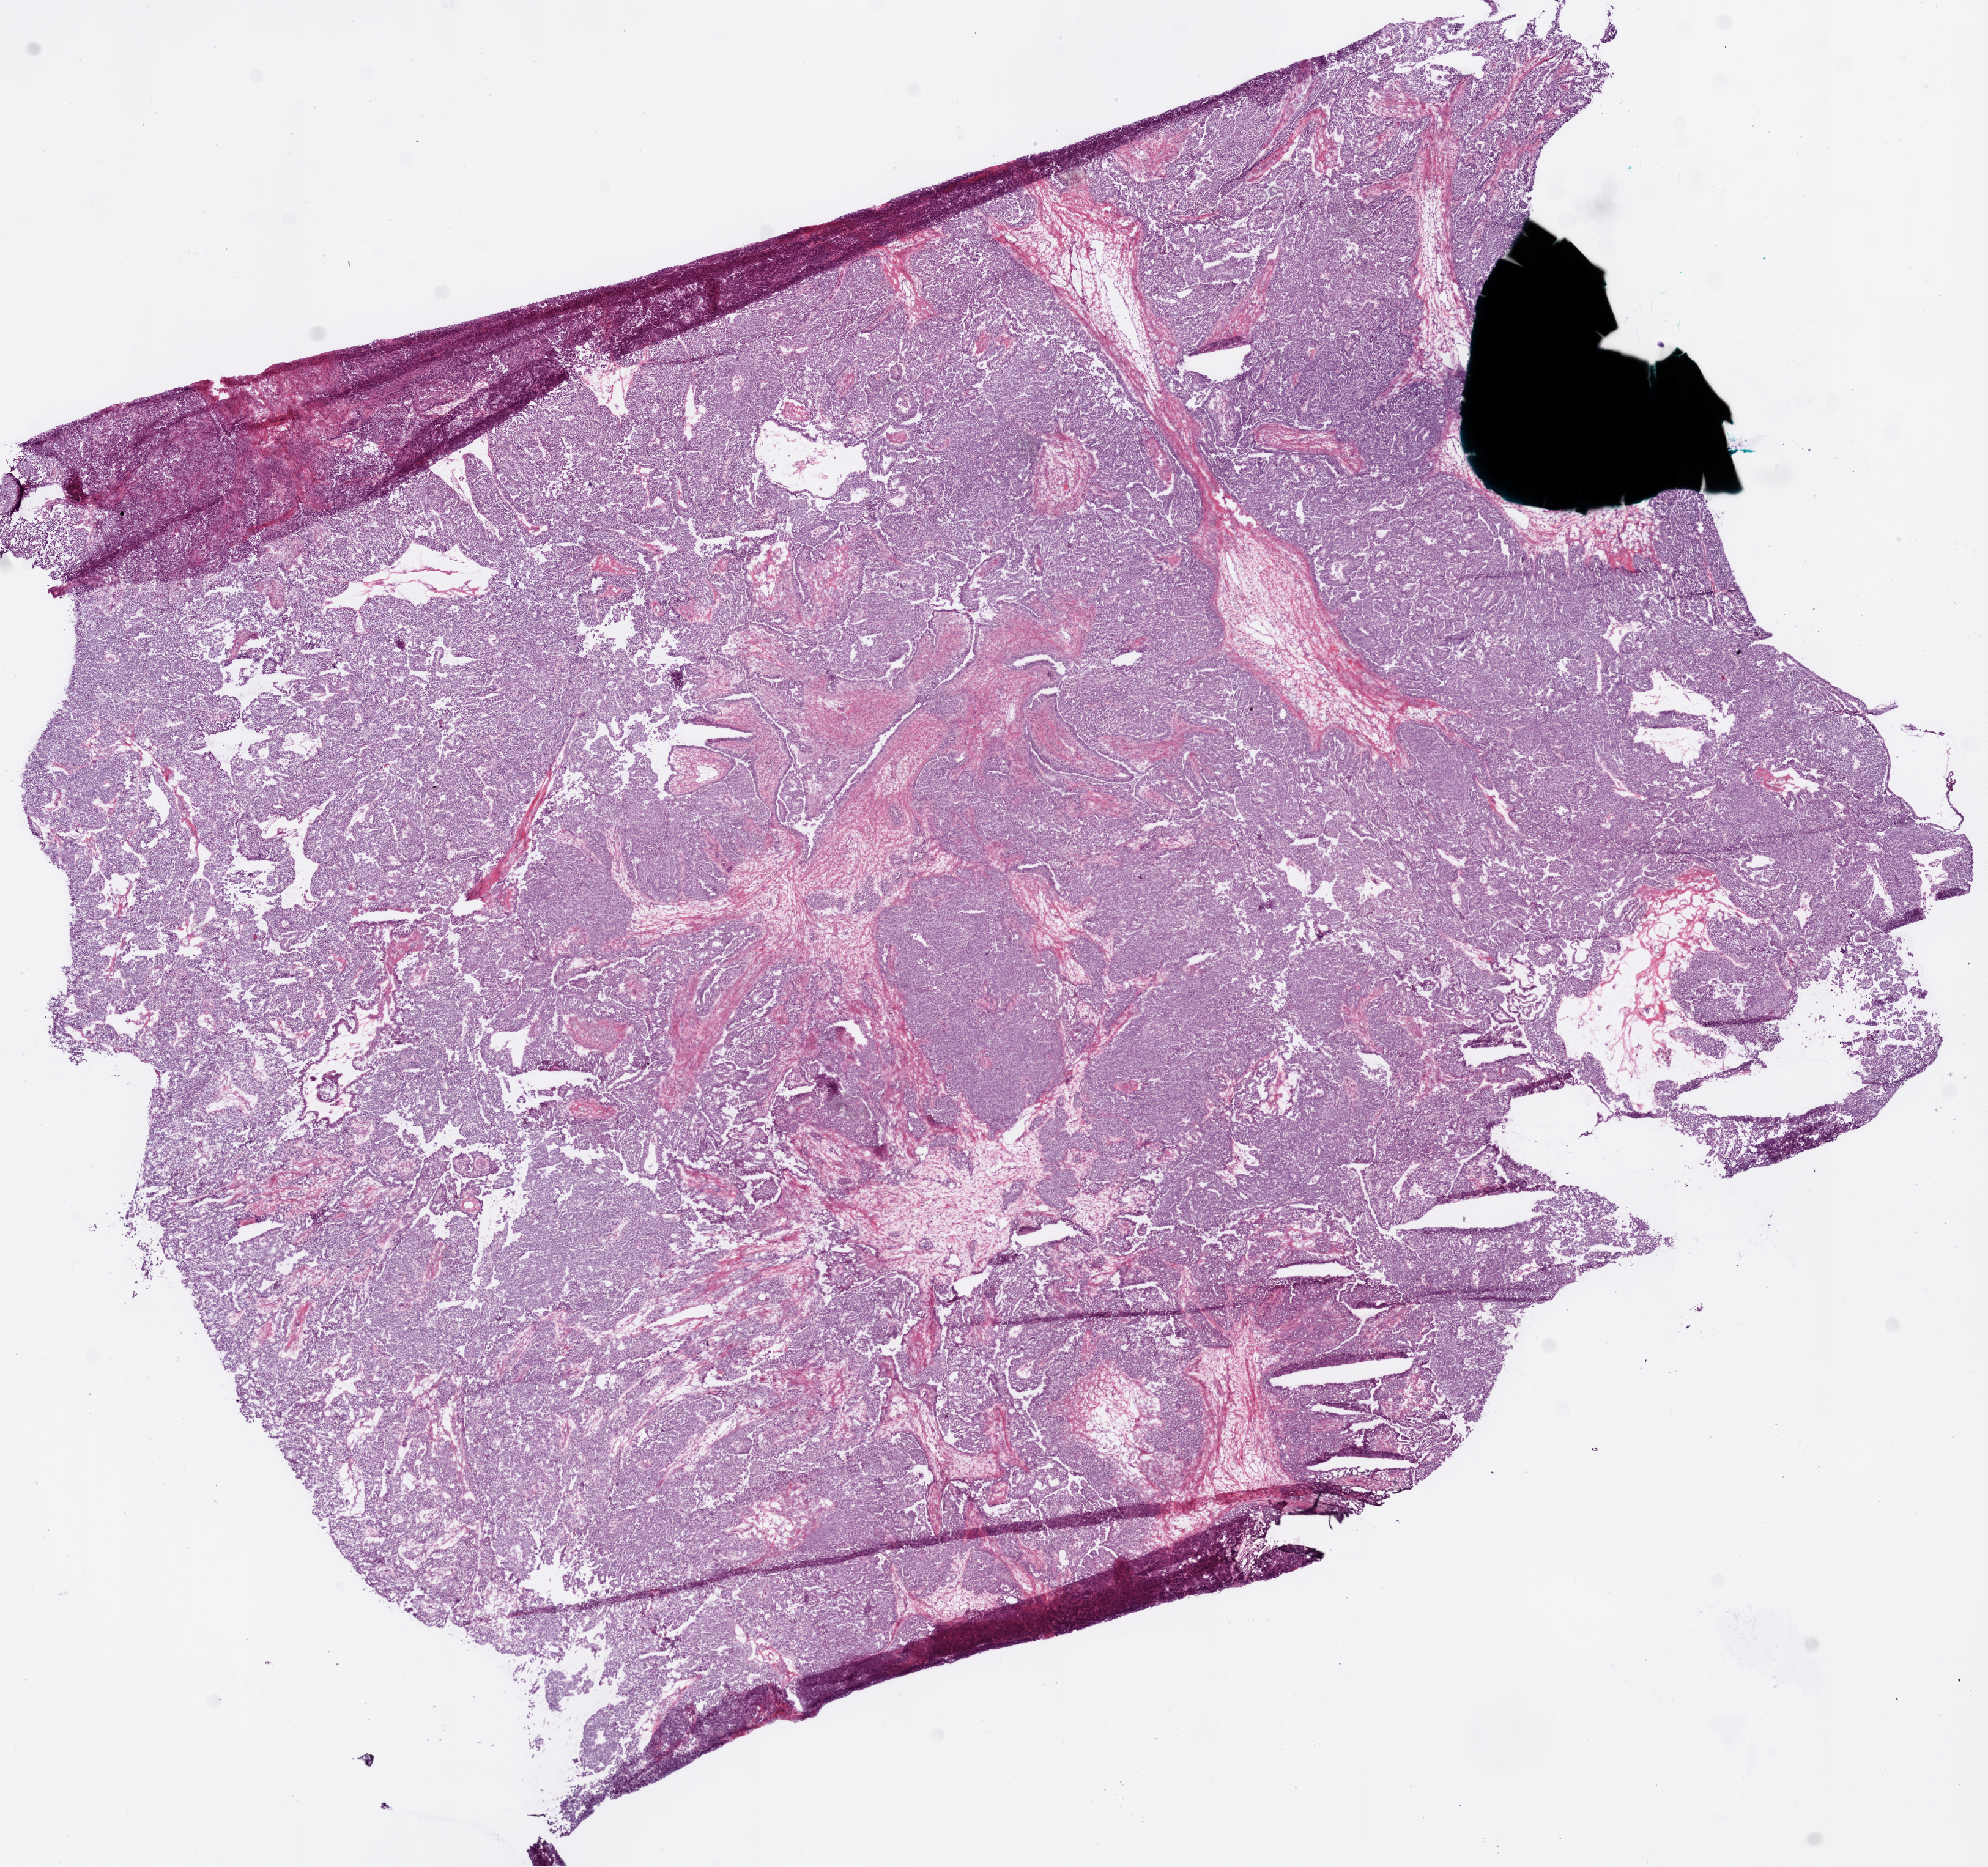
Digitized H&E-stained tissue section (whole slide) — a low-resolution overview of the entire scanned area, about 13.0 x 12.2 mm, frozen section from the bottom of the tissue portion, primary tumour sample from the ovary. Female, age 62 years at initial diagnosis. Histologic grade: G3 (poorly differentiated). Composition of this section per pathologist review: tumour cells 83%, tumour nuclei 90%, normal cells 15%, stromal cells 0%, necrosis 2%.
Laterality: bilateral. Histologic diagnosis: Serous cystadenocarcinoma, NOS. FIGO stage: IIIC.